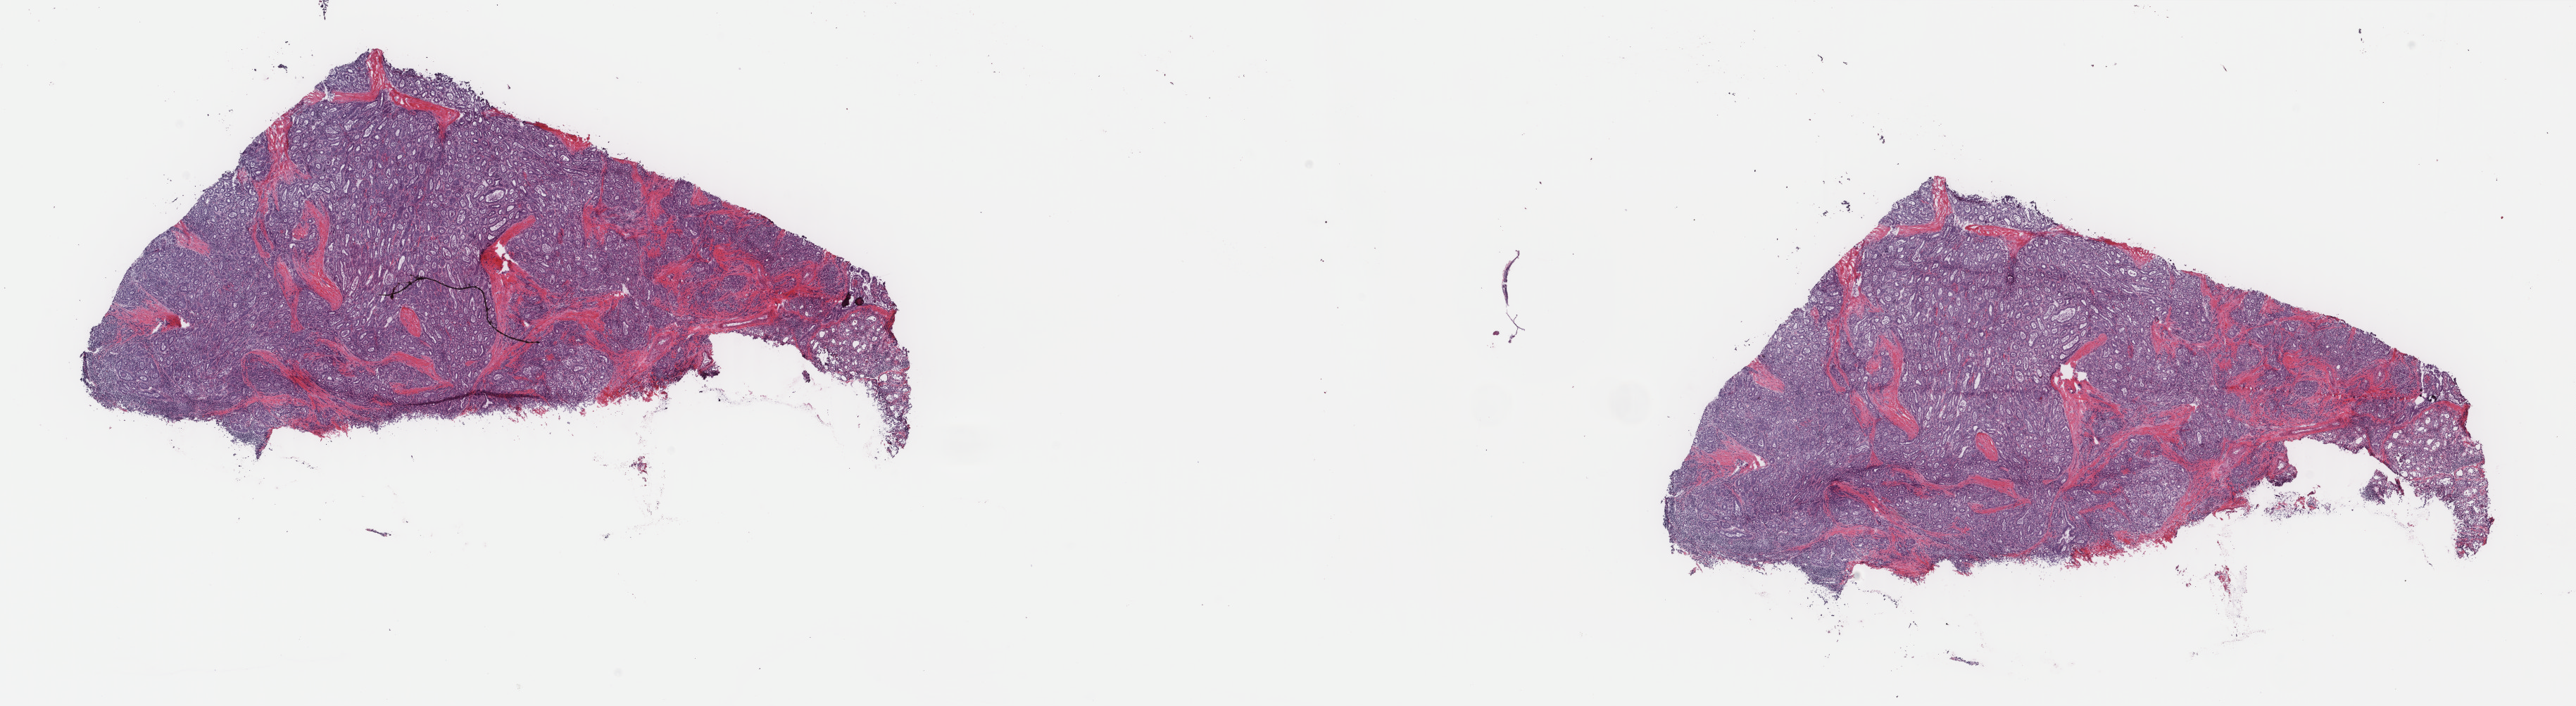
Whole-slide histology image, H&E-stained, shown as a low-resolution overview of the whole scanned area (about 29.0 x 8.0 mm). Frozen section from the top of the tissue portion. Primary tumour sample from the thyroid. Female, age 23 years at initial diagnosis. Pathologist review of this section (percent, as recorded): tumour cells 90%, tumour nuclei 80%, normal cells 5%, stromal cells 5%, necrosis 0%. Inflammatory infiltration, as recorded: lymphocyte infiltration 0%, monocyte infiltration 0%, neutrophil infiltration 0%.
Lymph nodes positive (case pathology): 1 of 4 examined. TNM: T2 N1a MX. AJCC pathologic stage: I (7th edition). Pathologic diagnosis: Papillary adenocarcinoma, NOS (thyroid gland).